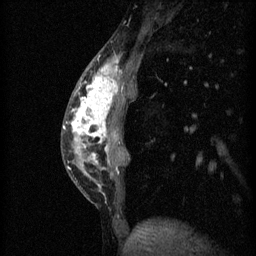
Breast MRI (dynamic contrast-enhanced), one sagittal slice; slice 16 of 60 in the series (ordered by position); 3 images stored at this slice position (order not interpretable as contrast timing); 1.5 T; TE 4.2 ms, TR 11 ms; 256 × 256 image matrix, field of view 180 × 180 mm. Patient: female, 40 years.
Structures marked on this image (semi-automatically segmented with operator editing):
- analysis volume of interest (the breast-tissue region the enhancement analysis was run in; not a lesion): bounding box [x1, y1, x2, y2] px = [63, 46, 136, 203]
- tumour enhancement mask (voxels above the 70 % enhancement threshold inside the analysis volume of interest): [65, 60, 119, 169]